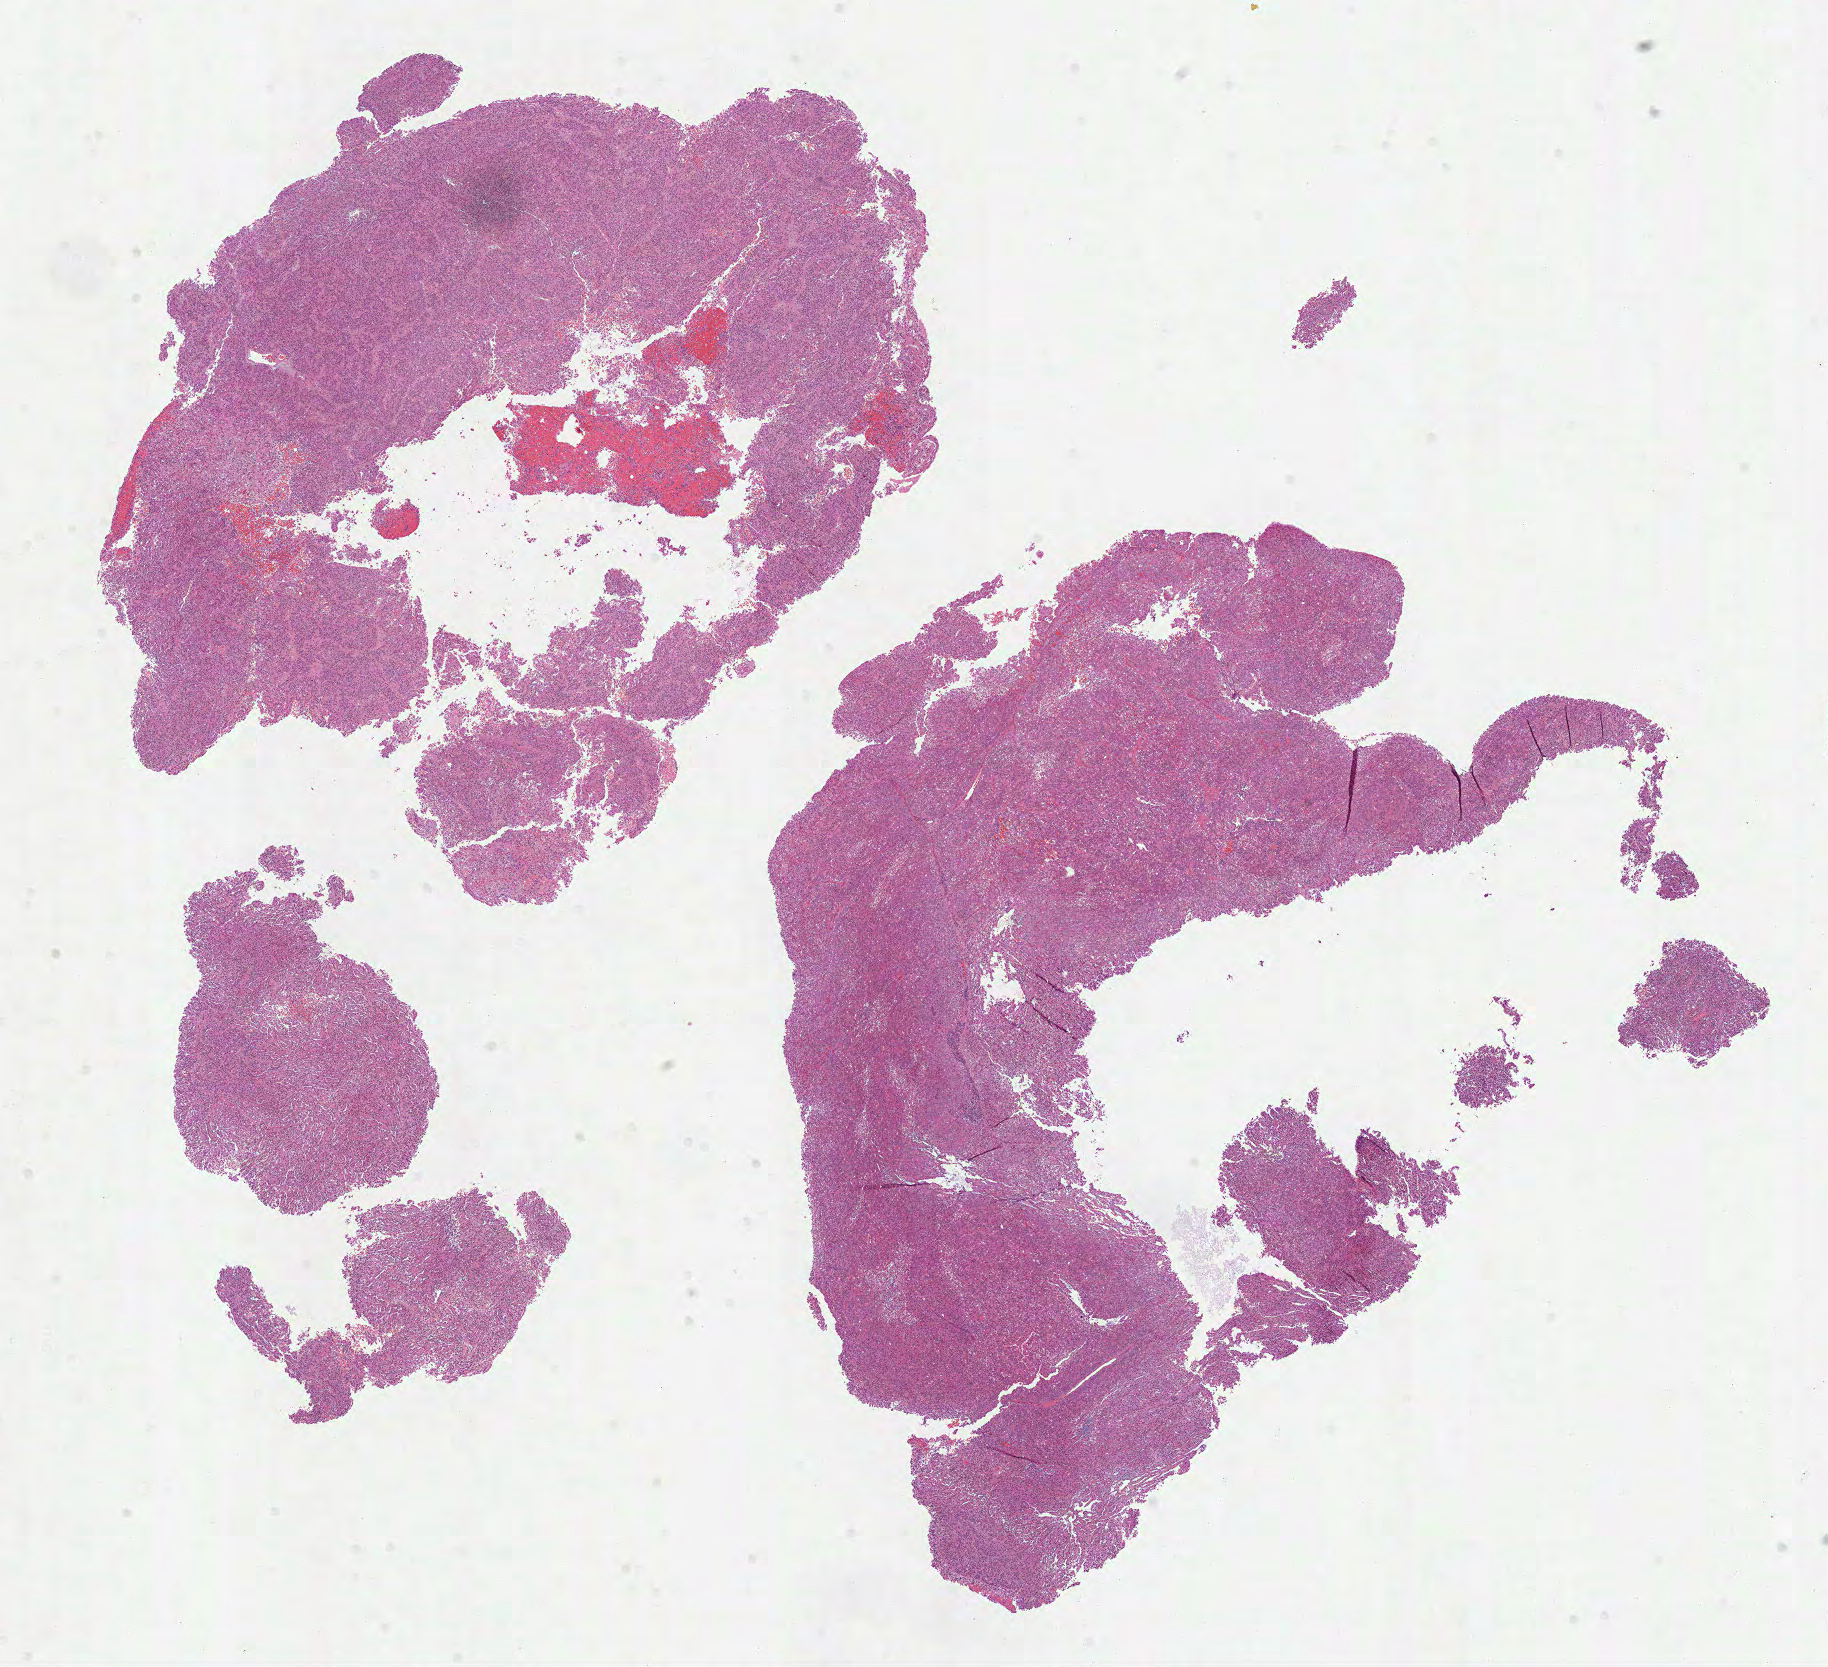
Digitized H&E tissue section (whole slide) — whole scanned area (about 14.7 x 13.4 mm) shown as a low-resolution overview; formalin-fixed paraffin-embedded (FFPE) diagnostic section; primary tumour sample from the kidney. Male patient; age at initial diagnosis 73 years.
AJCC pathologic stage: I. TNM: T1a NX MX. Diagnosis: Papillary adenocarcinoma, NOS.